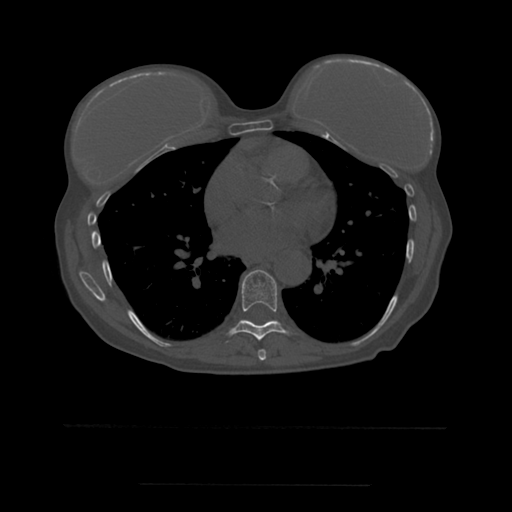
CT including the spine, one axial slice; position 340 of 544 along the scan axis; bone window (W 1800 / L 400 HU); 1.25 mm slice thickness; 512 × 512 image matrix, field of view 350 × 350 mm. Patient age 58 years. Case-level facts recorded for this patient, not image findings: primary cancer: lung.
Annotated regions visible in this slice (semi-automatically segmented with operator editing):
- T7 vertebra: bounding box <258,349,267,361> (left, top, right, bottom; pixels)
- T8 vertebra: <229,270,289,341>